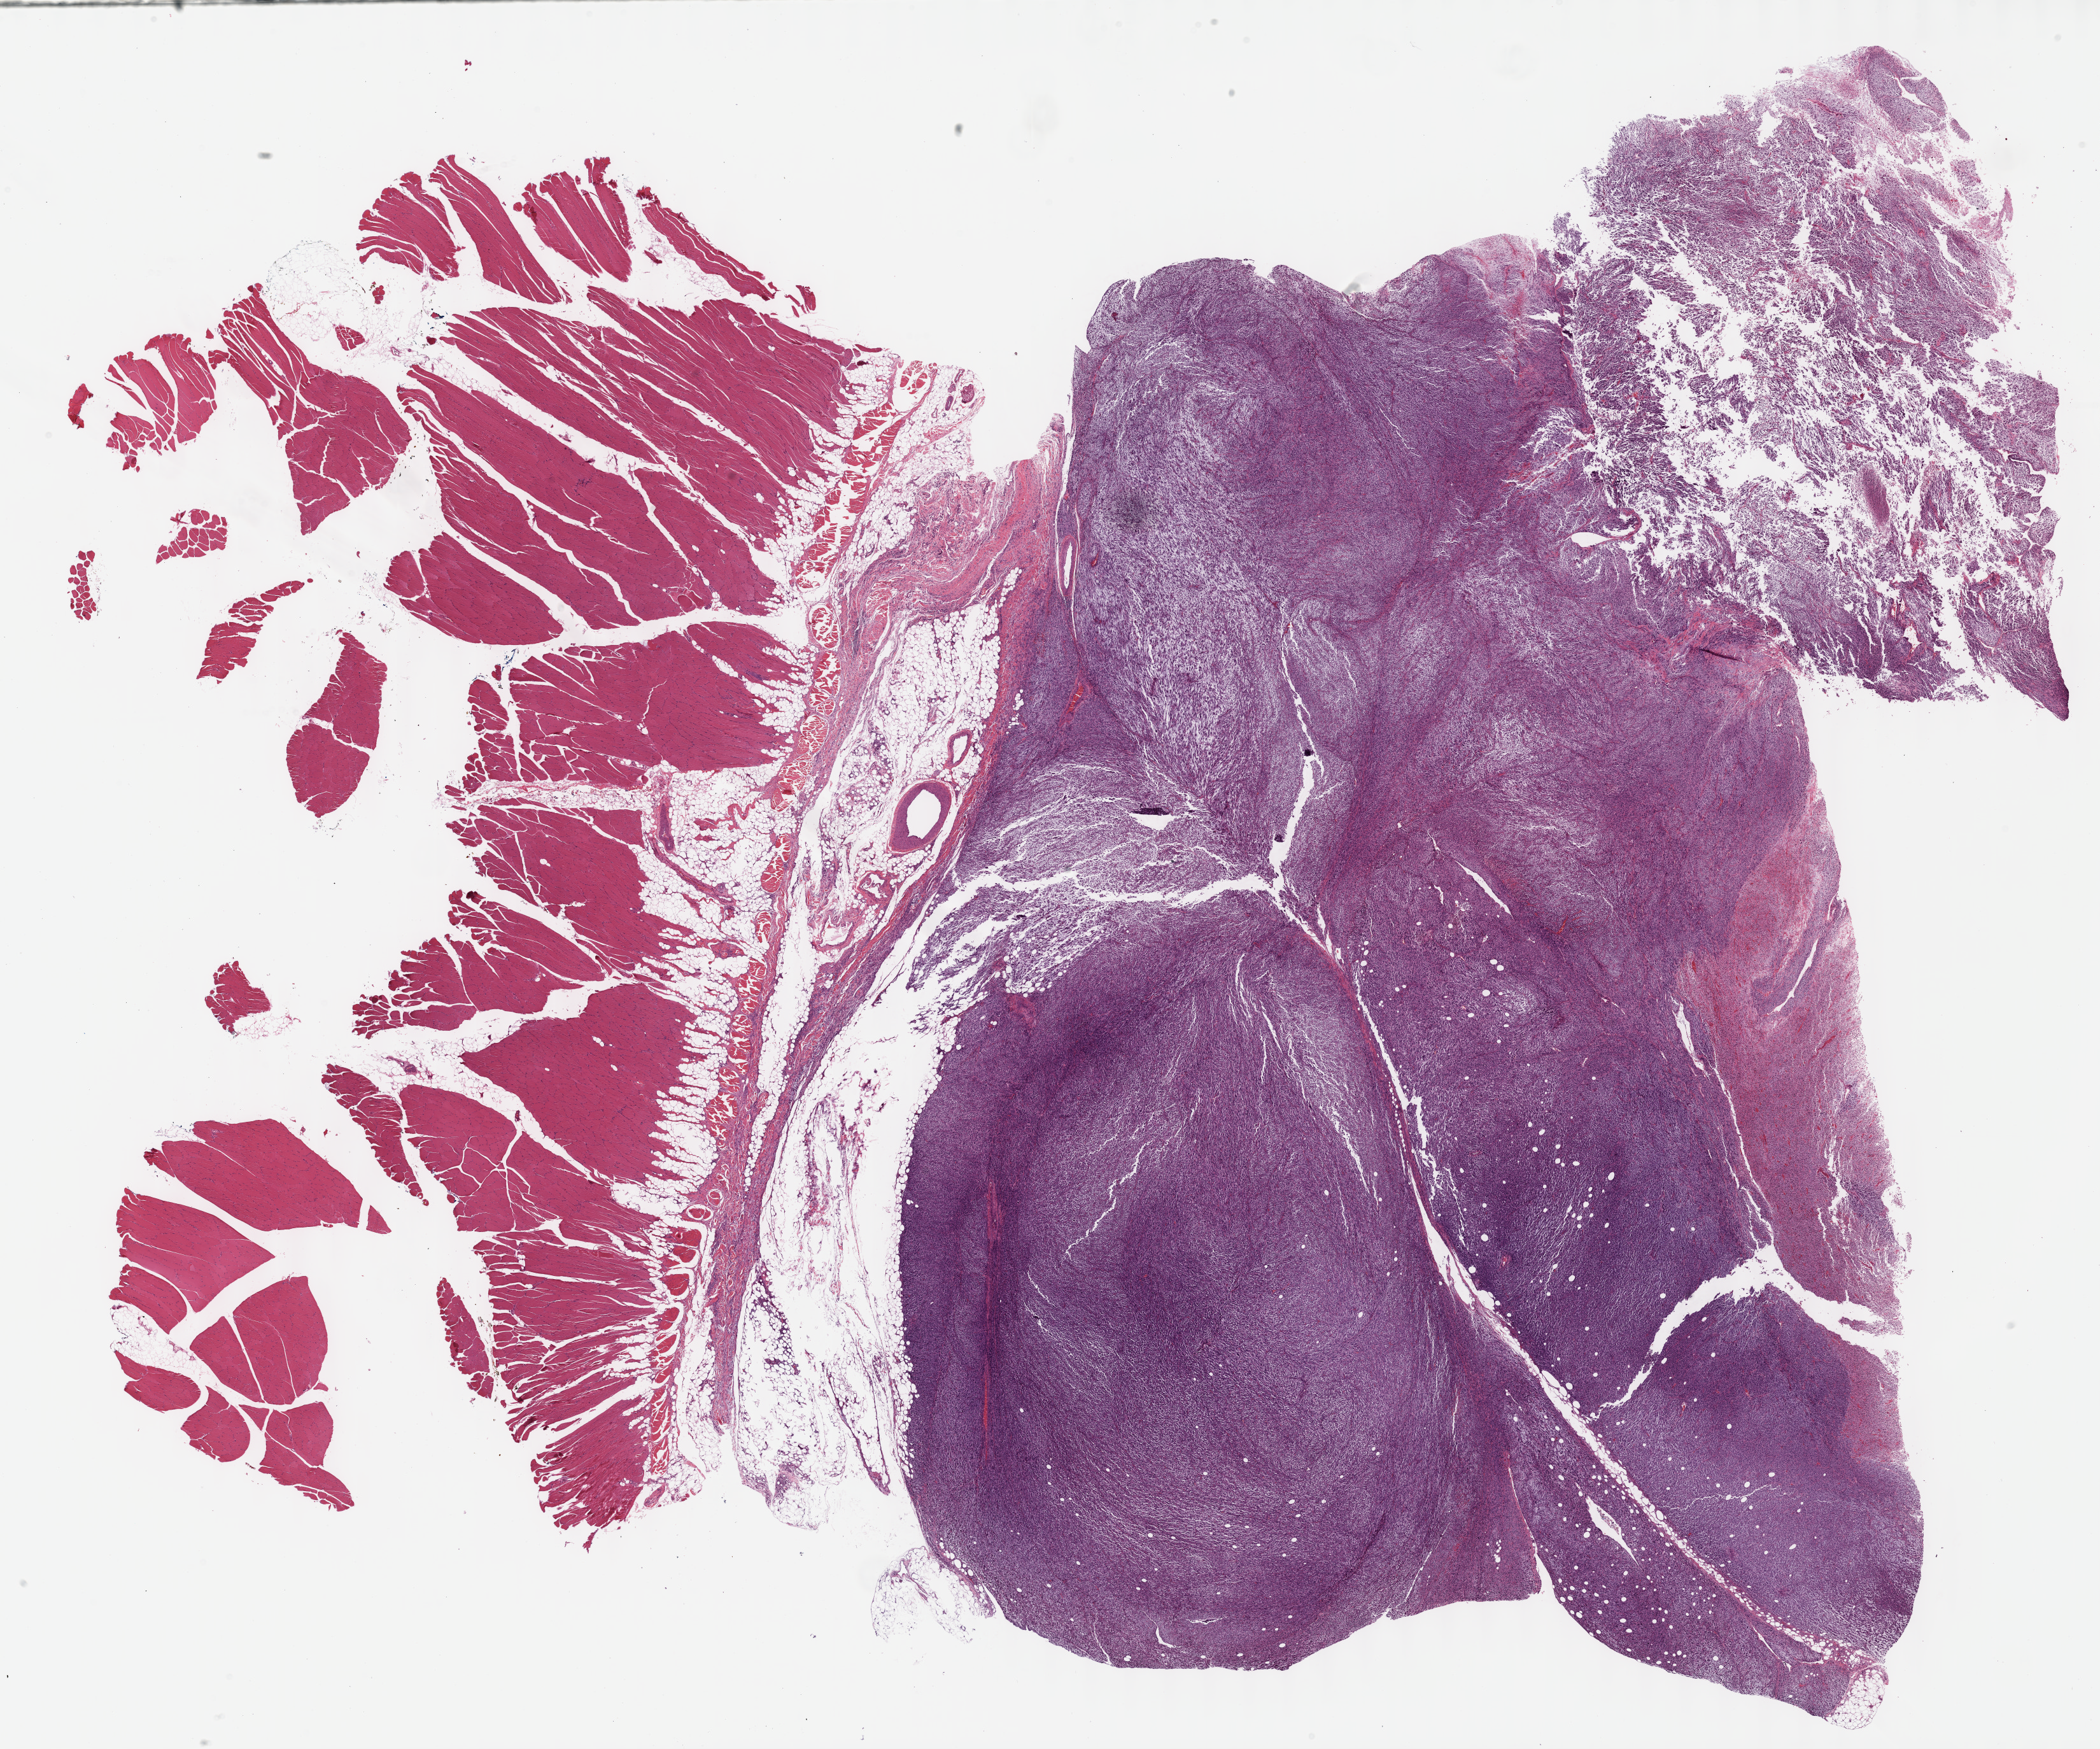
H&E-stained whole-slide image — low-resolution overview of the scanned area, about 26.7 x 22.2 mm (acquisition: 40x scan), formalin-fixed paraffin-embedded (FFPE) diagnostic section, primary tumour sample from the connective, subcutaneous and other soft tissues. Female patient; age at initial diagnosis 68 years.
Pathologic diagnosis: Fibromyxosarcoma (connective, subcutaneous and other soft tissues of lower limb and hip).